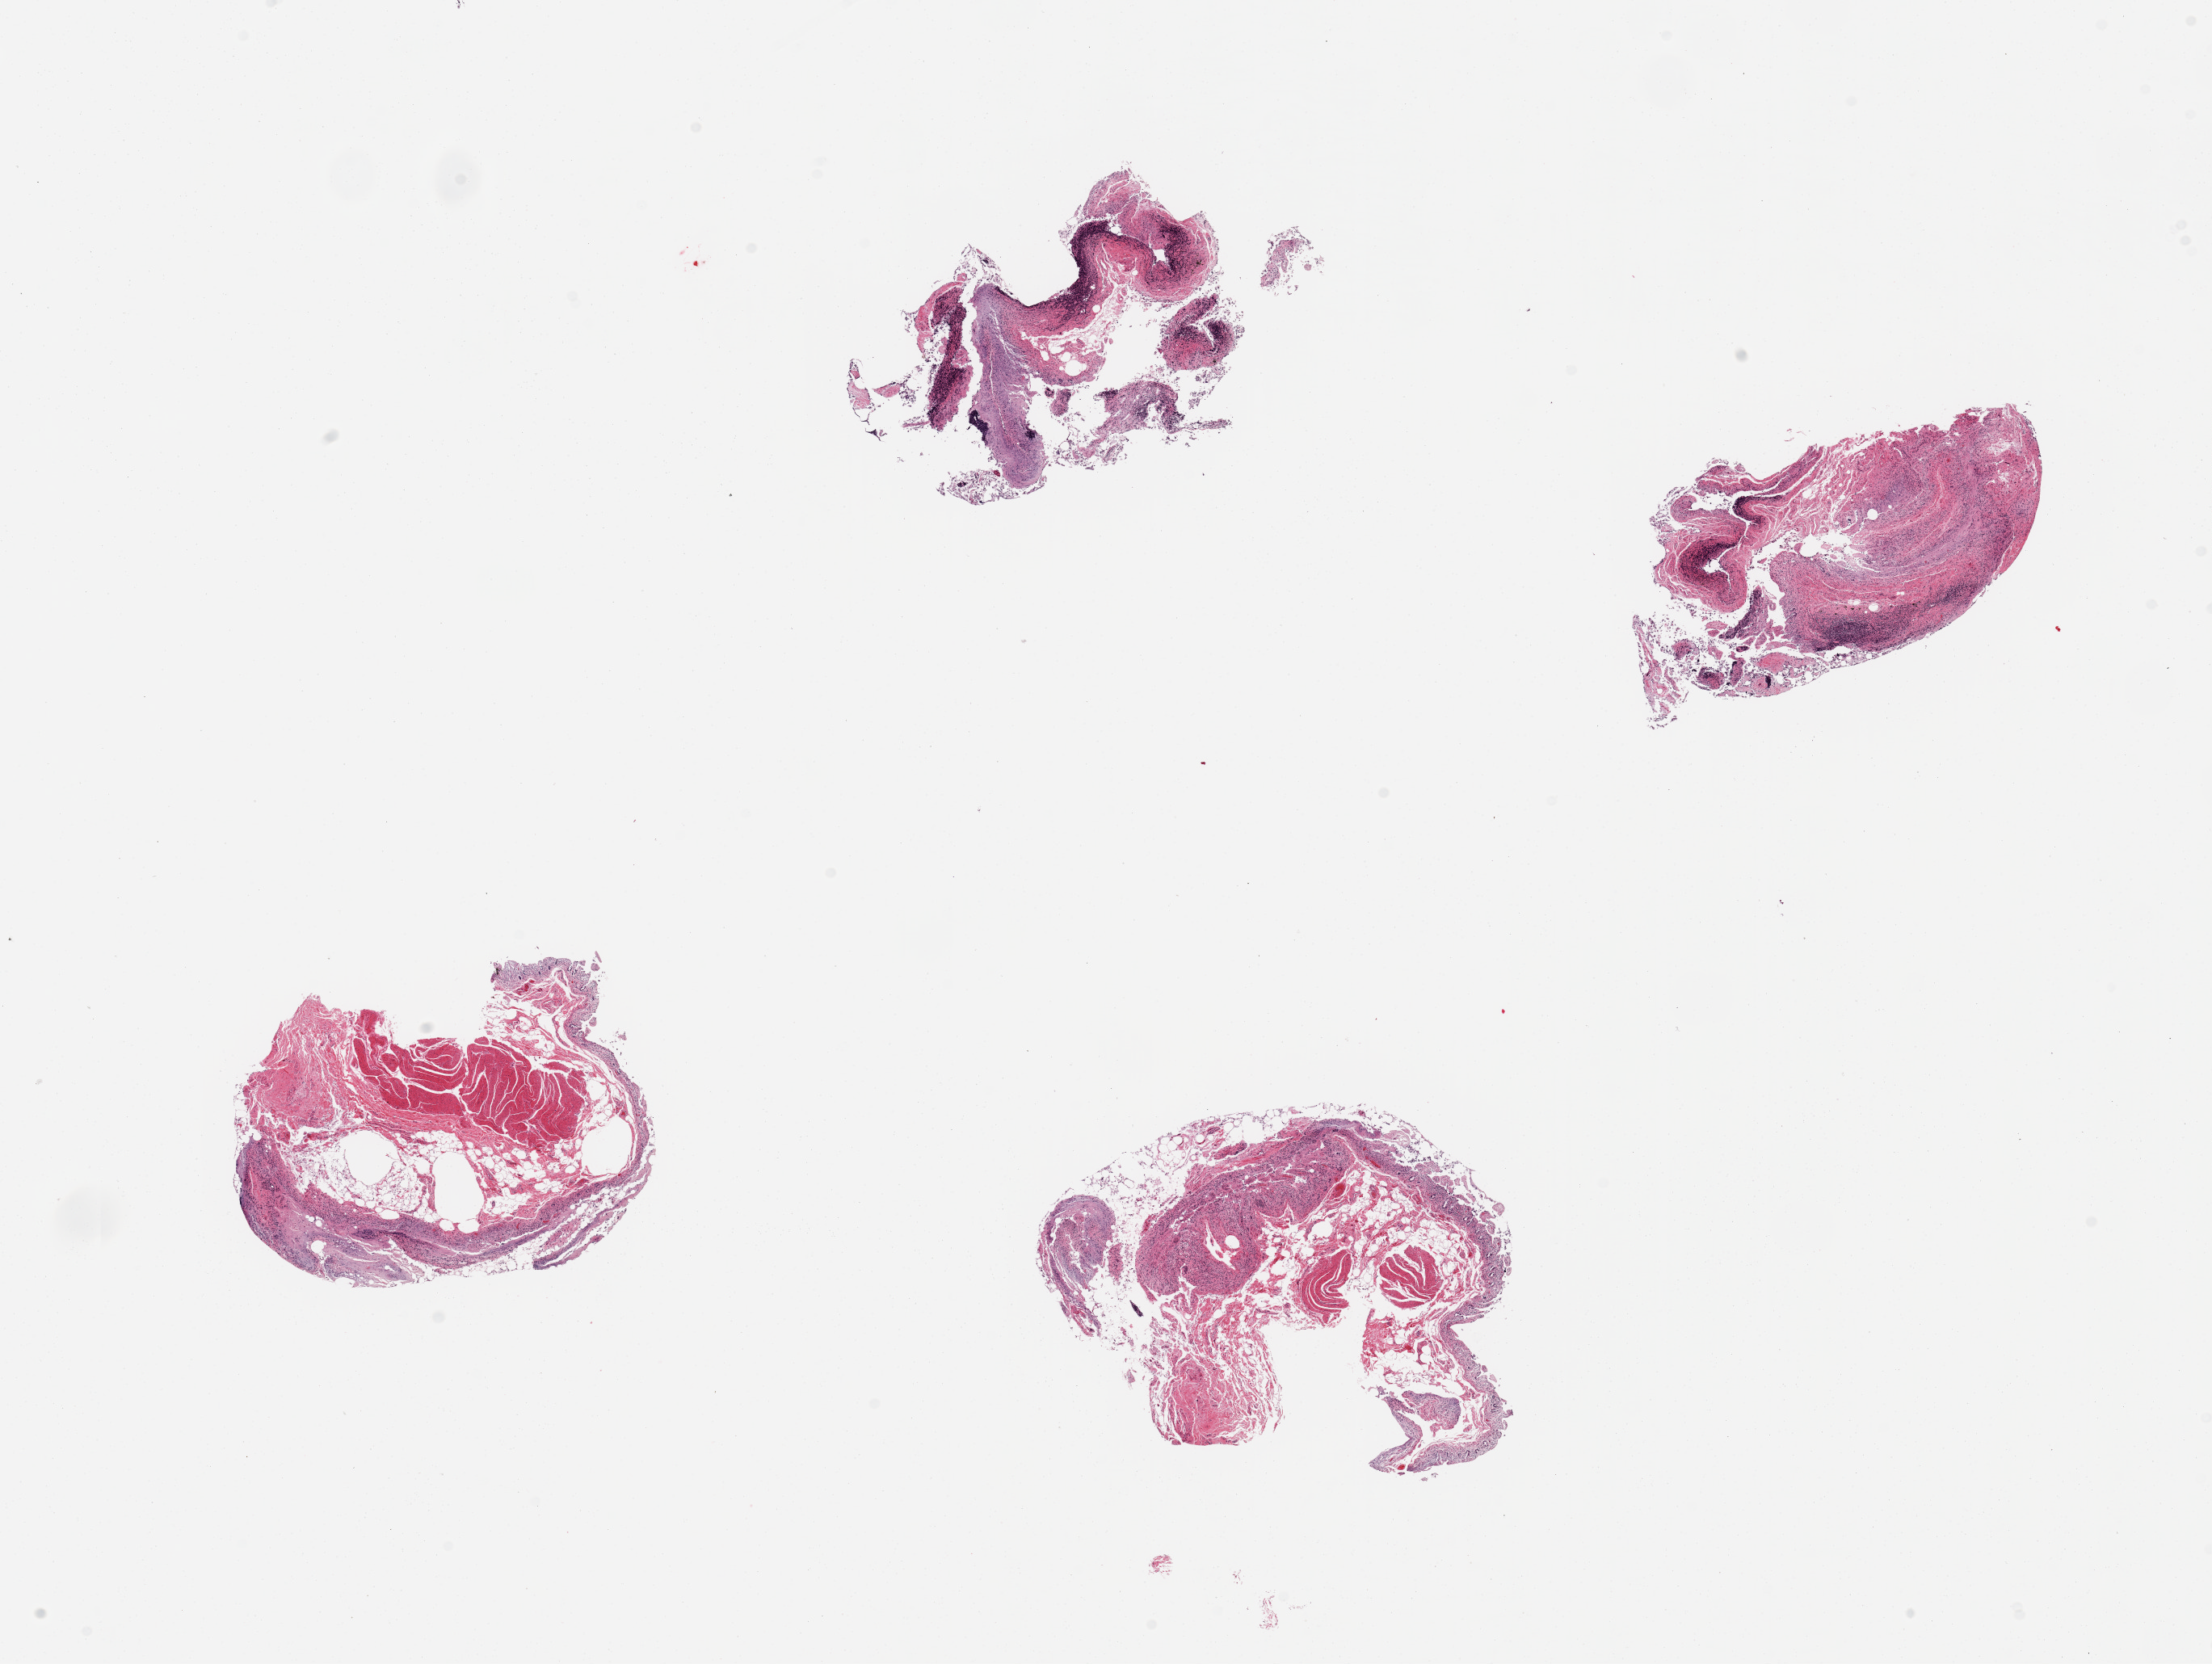
Whole-slide image, hematoxylin and eosin (H&E) stain, low-resolution overview of the scanned area, about 21.7 x 16.3 mm (from a 20x scan). PAXgene-fixed paraffin-embedded (PFPE) section. Target tissue: ileum. Donor tissue sample. Donor: female.
Pathologist's review note for this sample: 4 pieces, mucosa badly autolyzed, lymphoid aggregates remain, ~10% tota tisssue.